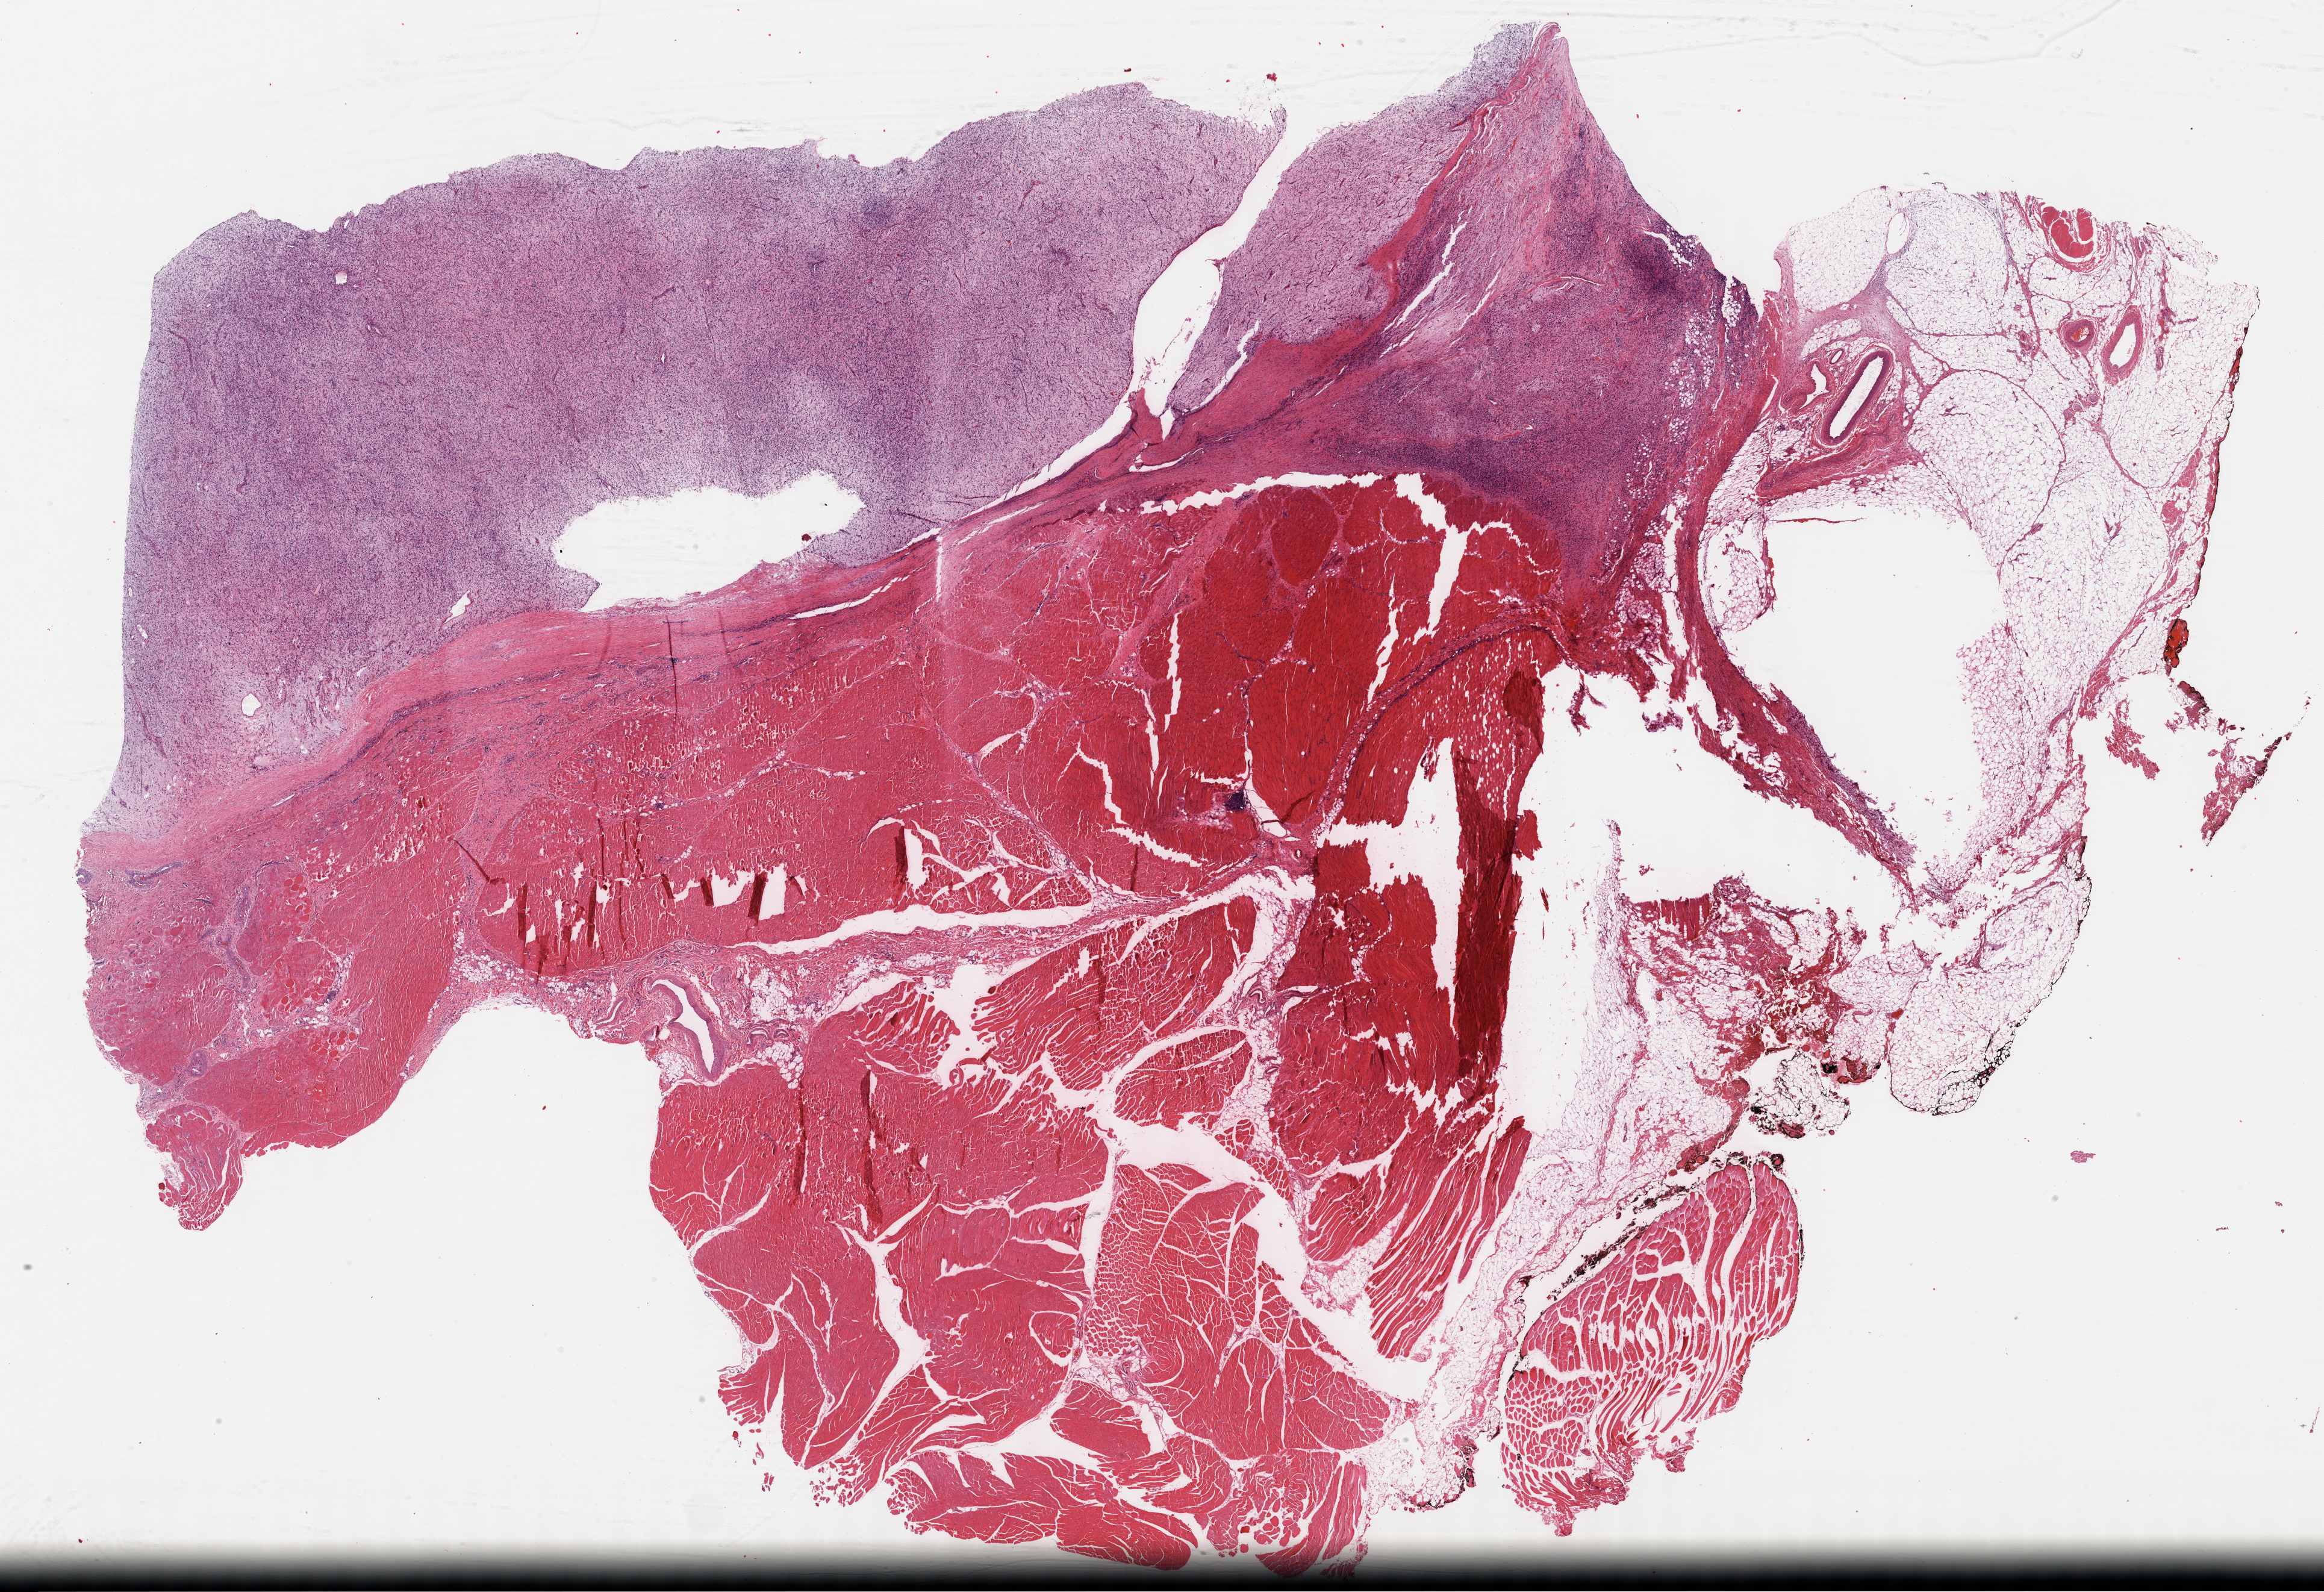
Hematoxylin and eosin (H&E) stained whole-slide image, shown as a low-resolution overview of the whole scanned area (about 31.2 x 21.4 mm), formalin-fixed paraffin-embedded (FFPE) diagnostic section, primary tumour sample from the connective, subcutaneous and other soft tissues. Patient: male, age at initial diagnosis 35 years.
• diagnosis: Fibromyxosarcoma